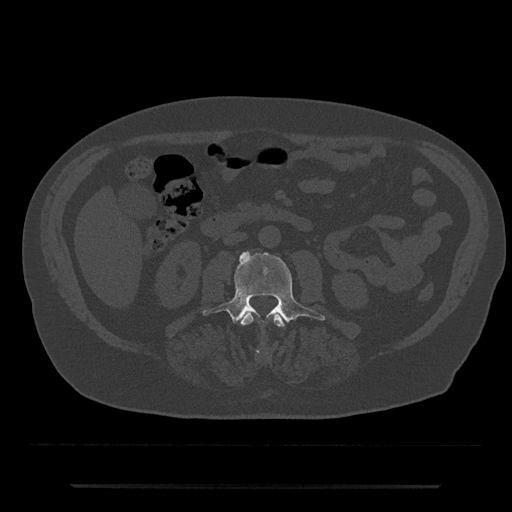
CT including the spine, one axial slice; slice 423 of 797 in the series (ordered by position); reconstruction kernel Br40s/3; bone window (W 1800 / L 400 HU); 0.5 mm slice thickness; 512 × 512 image matrix, field of view 434 × 434 mm. Patient: male, 80 years. From the clinical record (not read from this slice): primary cancer: prostate; vertebrae with lytic lesions (as recorded): L1, T11.
Annotated regions visible in this slice (semi-automatically segmented with operator editing):
- L2 vertebra: bounding box (x1, y1, x2, y2) in pixels: (241, 312, 284, 353)
- L3 vertebra: (202, 251, 325, 323)